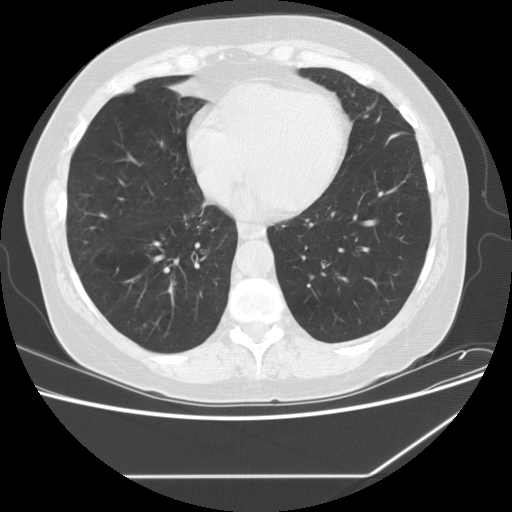
Low-dose screening chest CT, axial slice. Second screening round (one year after baseline). Lung window (W 1500 / L -600 HU). 2.5 mm slice thickness. 120 kVp. Slice 106 of 162 in the series. Female, age 59 years at enrolment. Current smoker at enrolment.
Expert-annotated lung lesion, bounding box (x1, y1, x2, y2) in pixels: (122, 311, 164, 348). No non-calcified nodule or mass ≥4 mm was recorded by the screening reader at this exam. Official screen result: negative screen, significant abnormalities not suspicious for lung cancer.